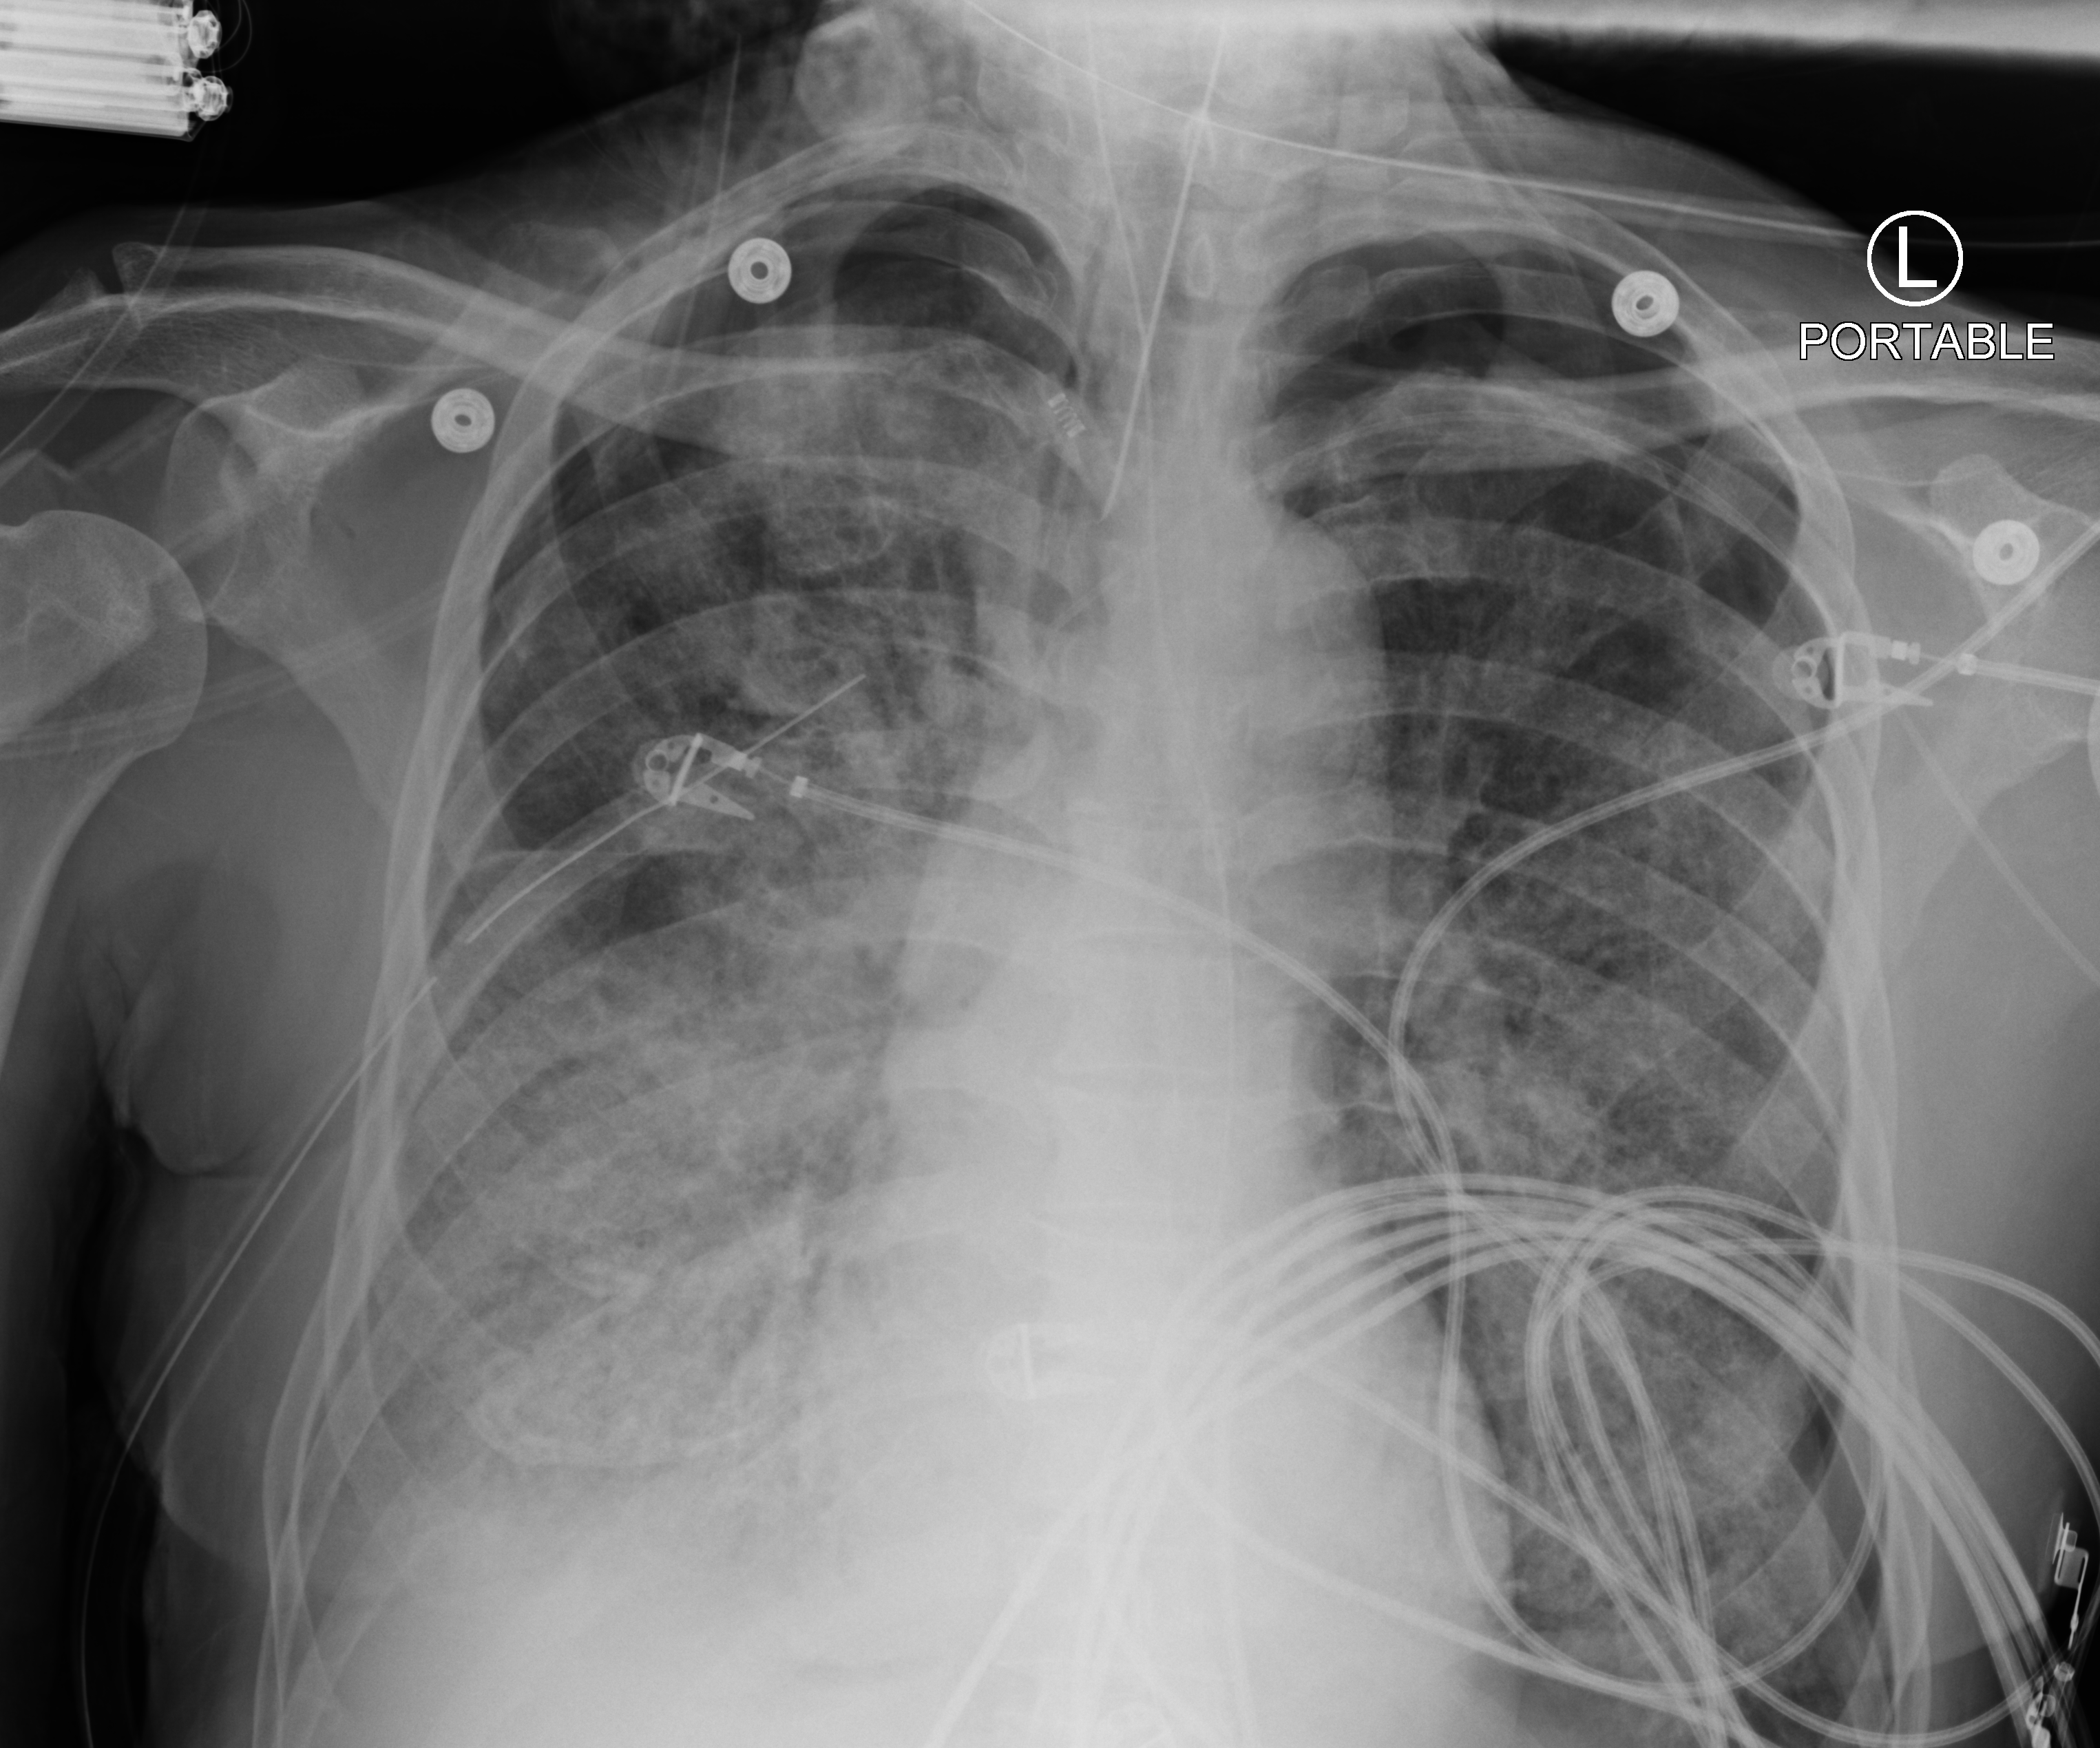
Portable chest radiograph; anteroposterior (AP) projection. Male patient hospitalised with COVID-19, age 60–74 years.
Hospital-stay facts (about this admission, not read from this image; timing relative to this image not recorded):
- mechanically ventilated during this hospital stay: yes
- other chronic lung disease (admission record): no